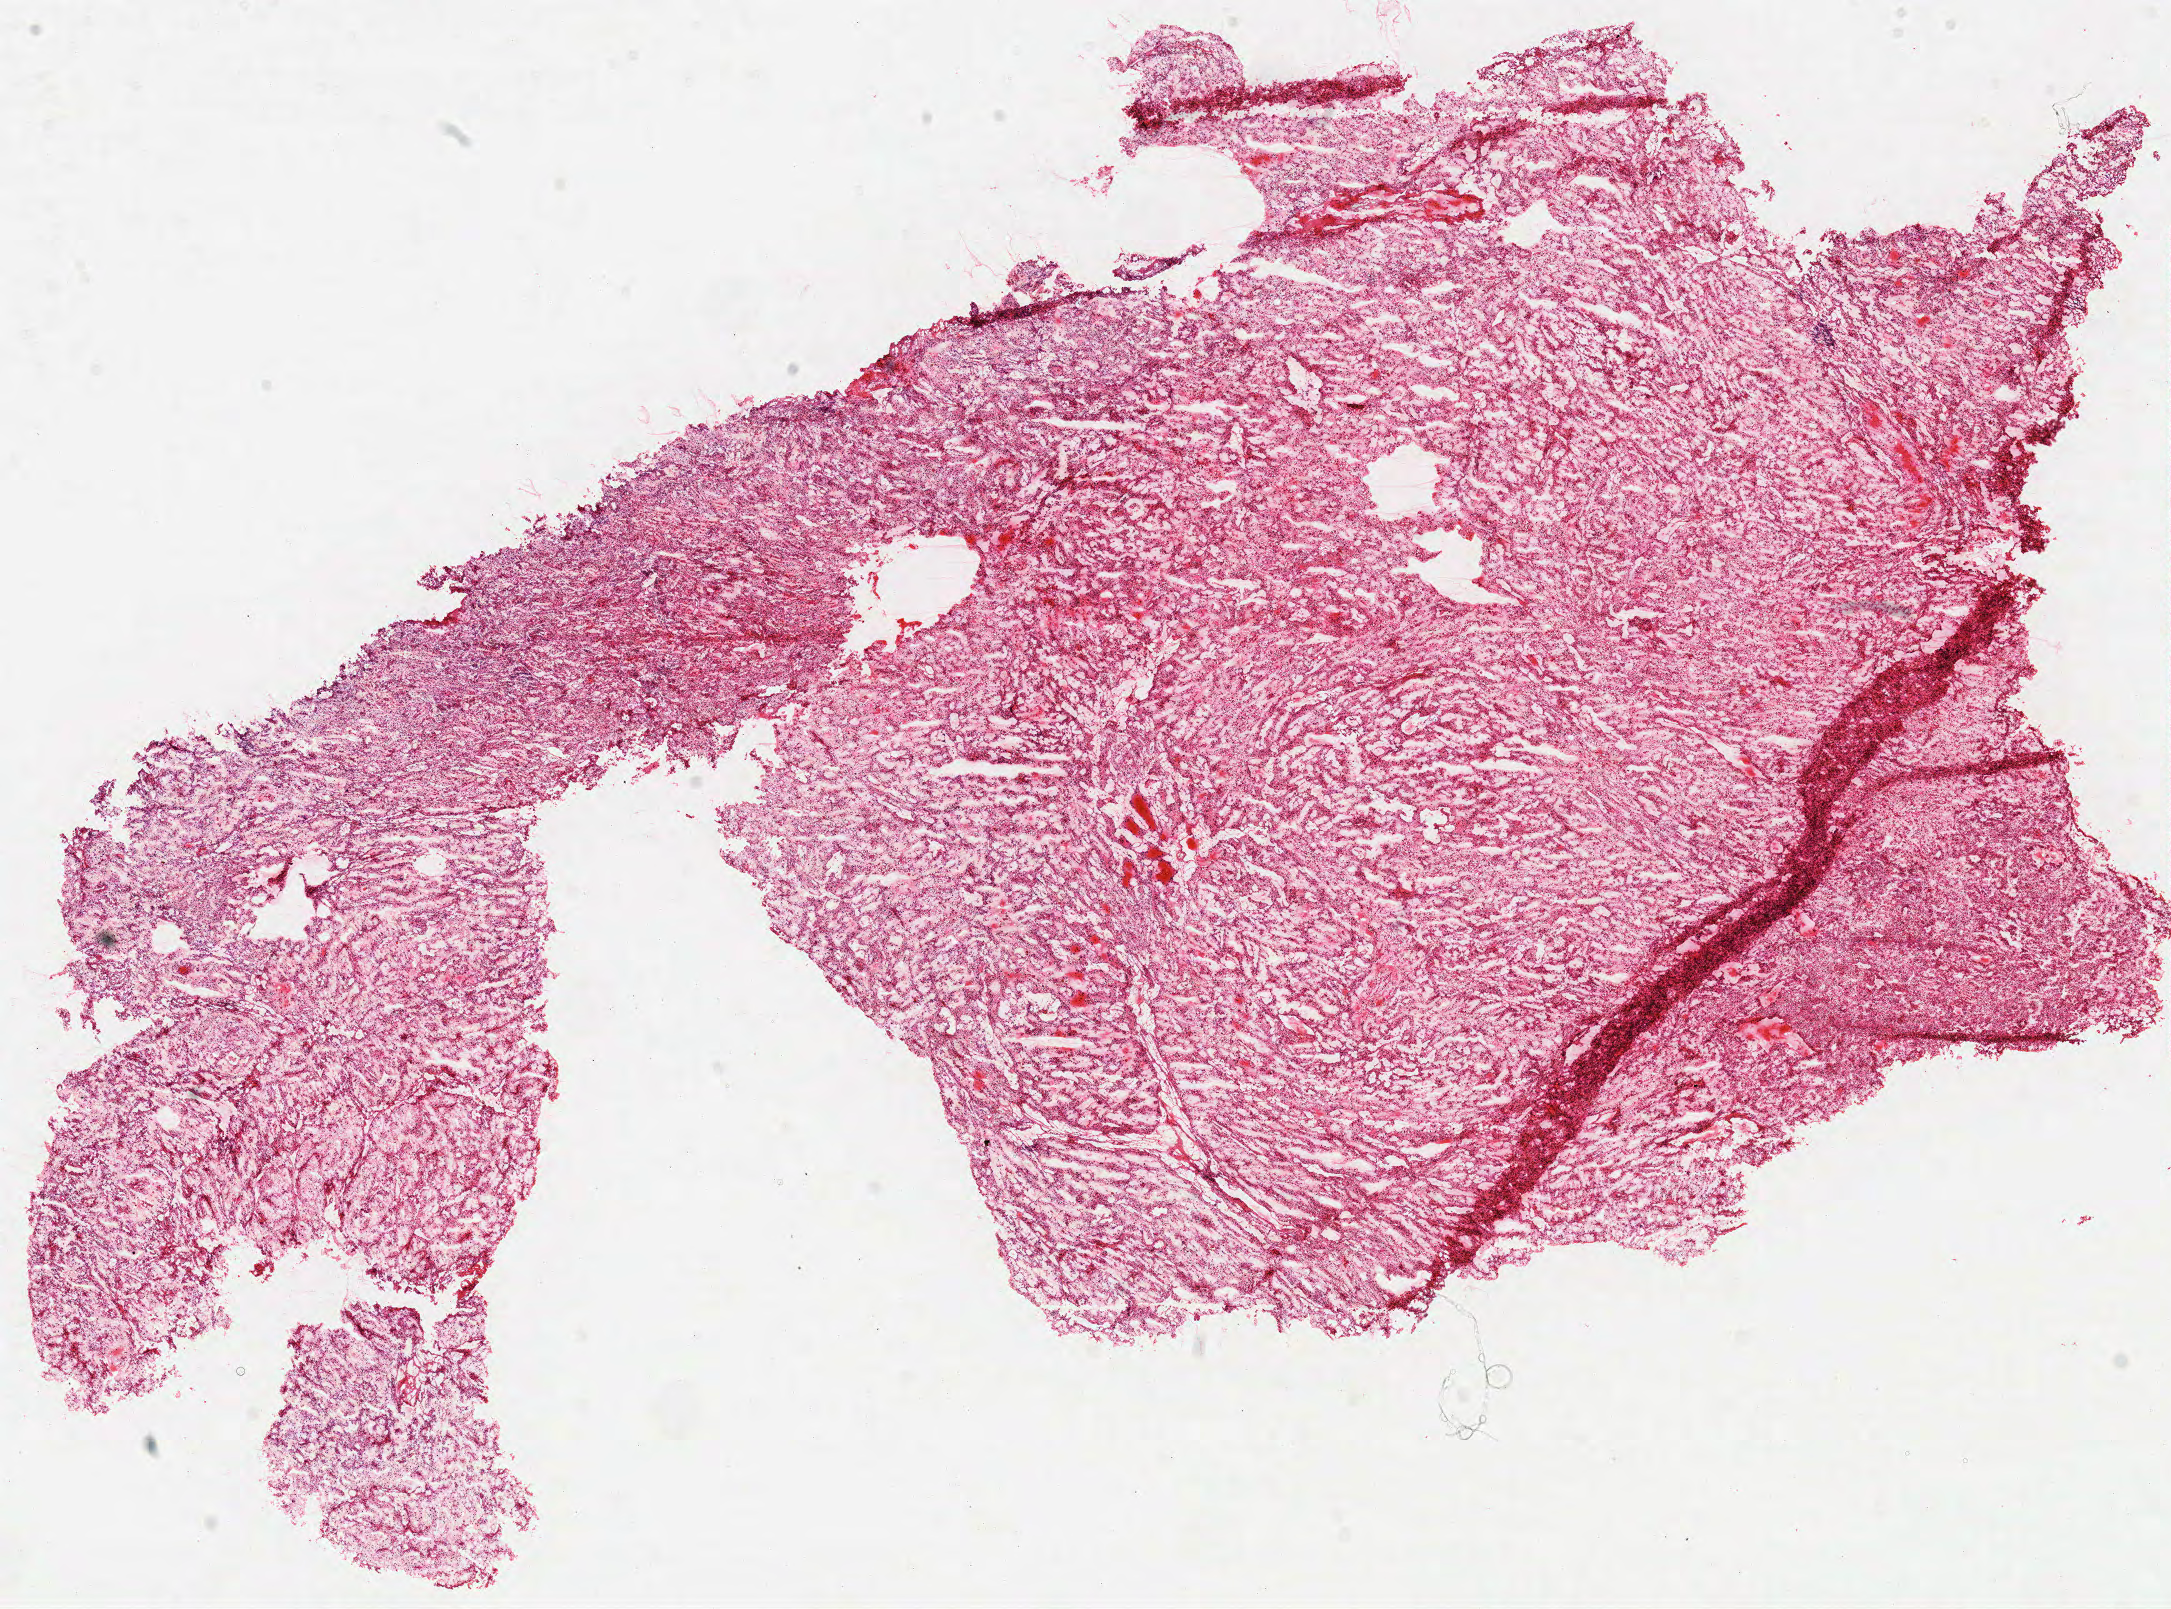
Whole-slide histology image, Hematoxylin and eosin (H&E) stained — whole scanned area (about 17.1 x 12.7 mm) shown as a low-resolution overview. Frozen section from the top of the tissue portion. Sample: primary tumour, kidney. Male, age 58 years at initial diagnosis. Histologic grade: G2 (moderately differentiated). Slide review estimates, as recorded: tumour cells 90%, tumour nuclei 85%, normal cells 0%, stromal cells 10%, necrosis 0%.
AJCC pathologic stage: II. Lymph nodes positive (case pathology): 0 of 5 examined. Diagnosis: Clear cell adenocarcinoma, NOS.